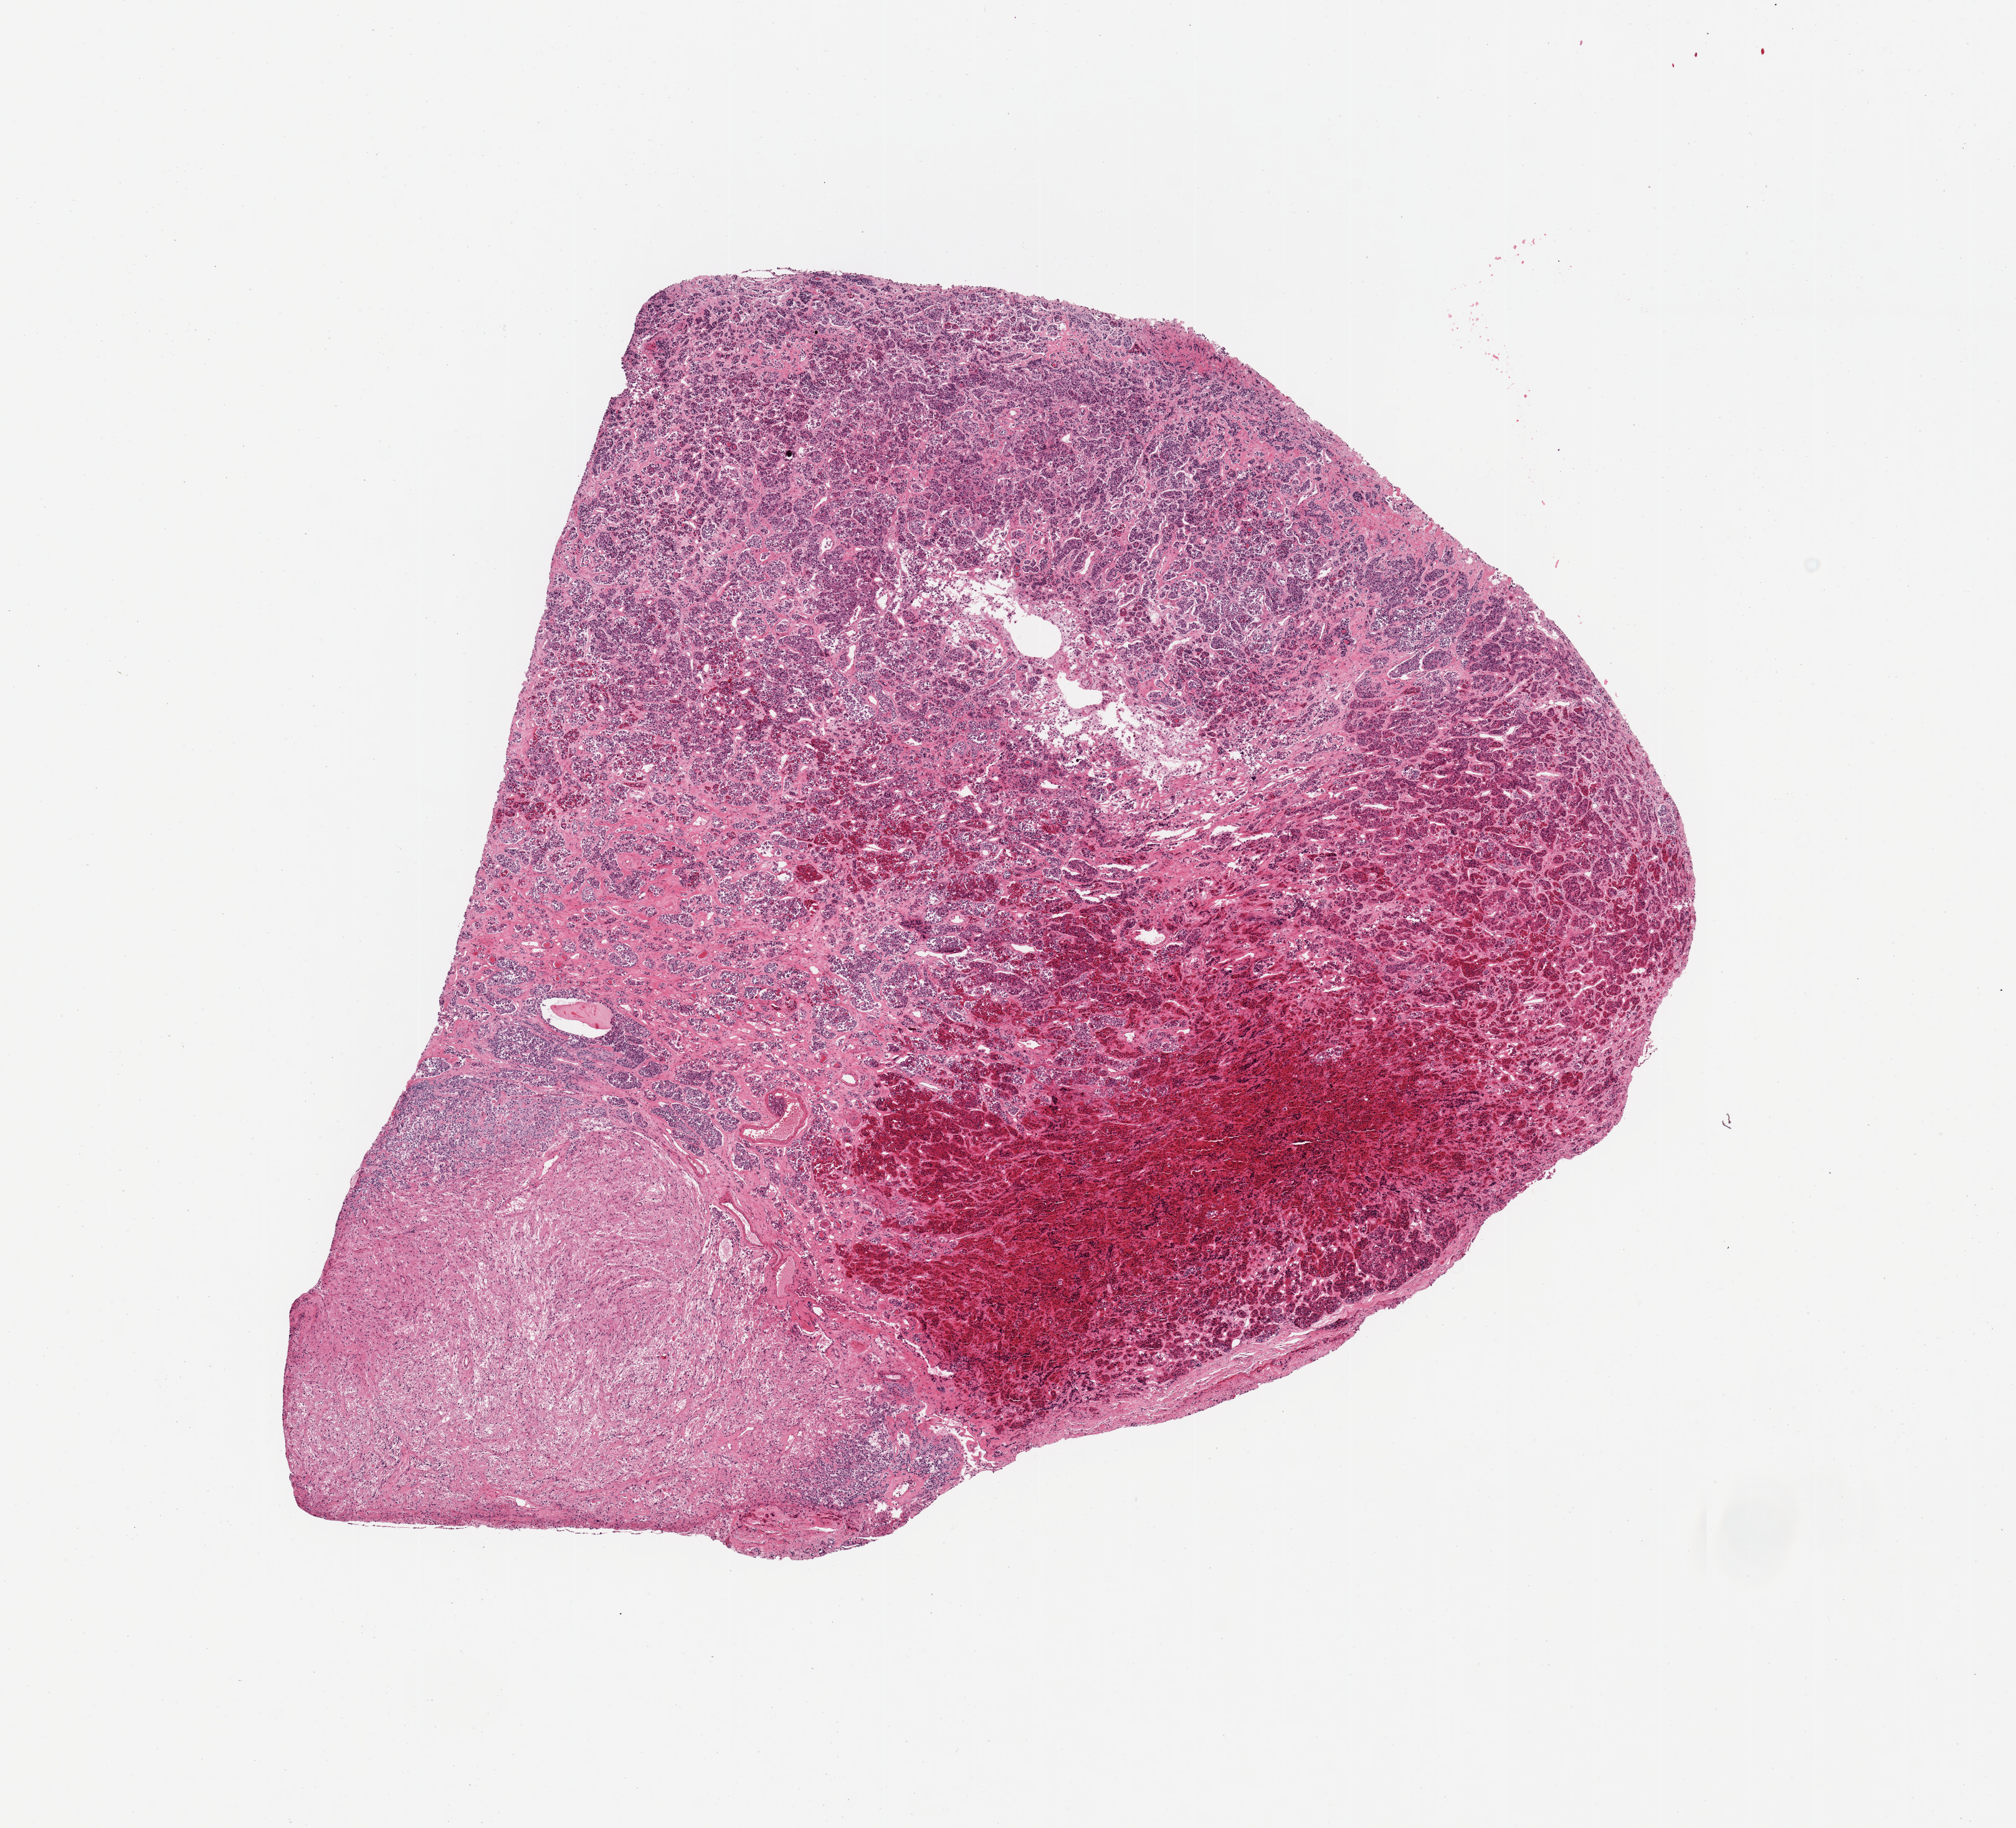
Whole-slide image, haematoxylin and eosin stain, low-resolution overview of the scanned area, about 12.8 x 11.6 mm. PAXgene-fixed paraffin-embedded (PFPE) section. Sampled site (target tissue): pituitary. Tissue donor sample. Male donor.
Review note (as recorded): 1 piece, mainly adenohypophysis, adherent ~3x3mm neurohypophysis.